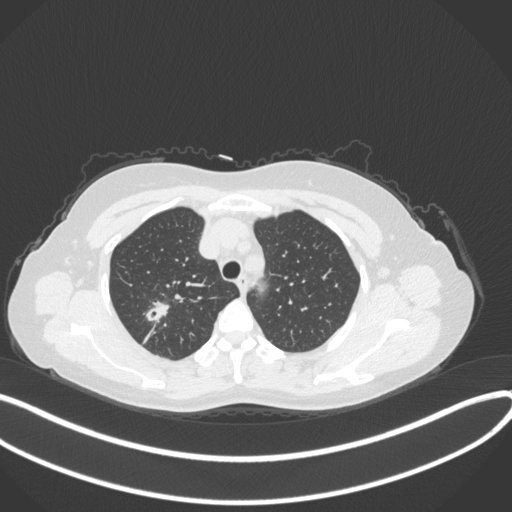
Chest CT, one axial slice. Slice 288 of 342 in the series (ordered by position). Reconstruction kernel B31f. 120 kVp. Lung window (W 1500 / L -600 HU). 1 mm slice thickness. 512 × 512 image matrix, field of view 400 × 400 mm. Female patient, age 50 years. From the clinical record (not read from this slice): clinical TNM (as recorded): T1c N0 M0.
Outlined on this slice (bounding box drawn by a radiologist):
- lung tumour (recorded histology: adenocarcinoma): bounding box (x1, y1, x2, y2) in pixels: (144, 293, 171, 326)